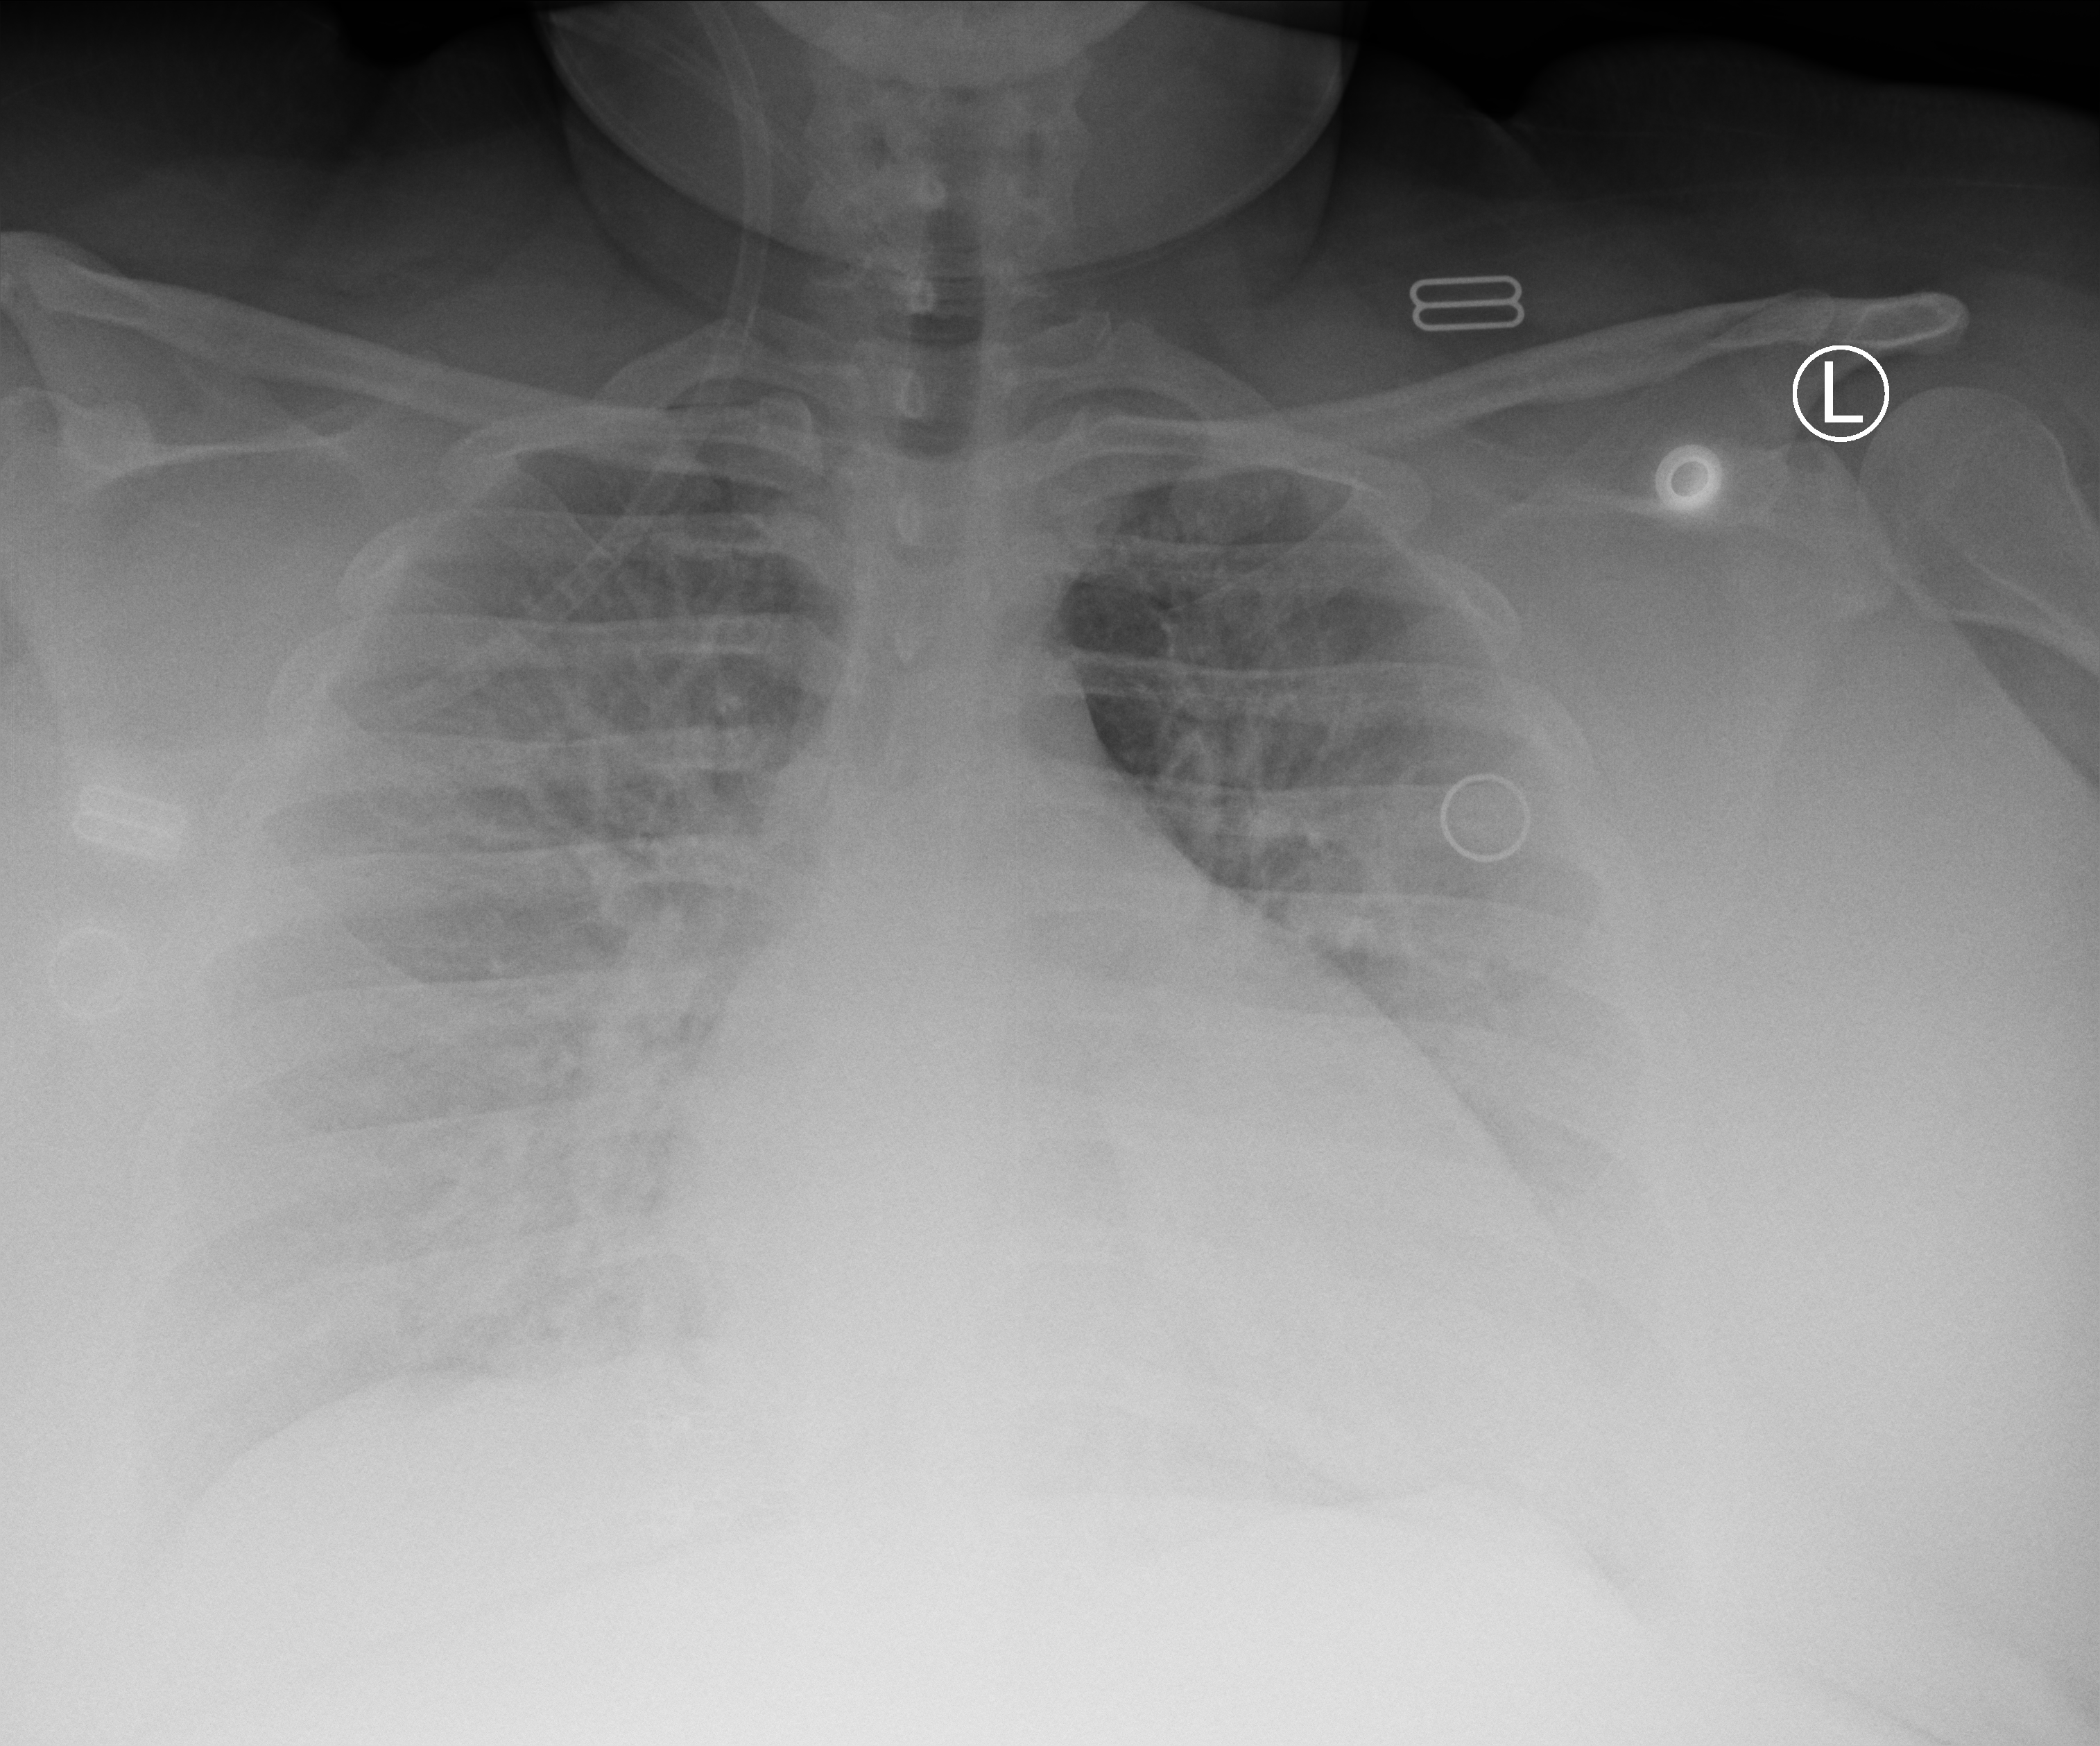
Bedside chest radiograph (computed radiography); anteroposterior (AP) projection. Female patient hospitalised with COVID-19, age 18–59 years.
Admission-level facts for this patient (not findings on this image; timing relative to this image not recorded): hypertension (admission record): no; length of hospital stay: 7 days.